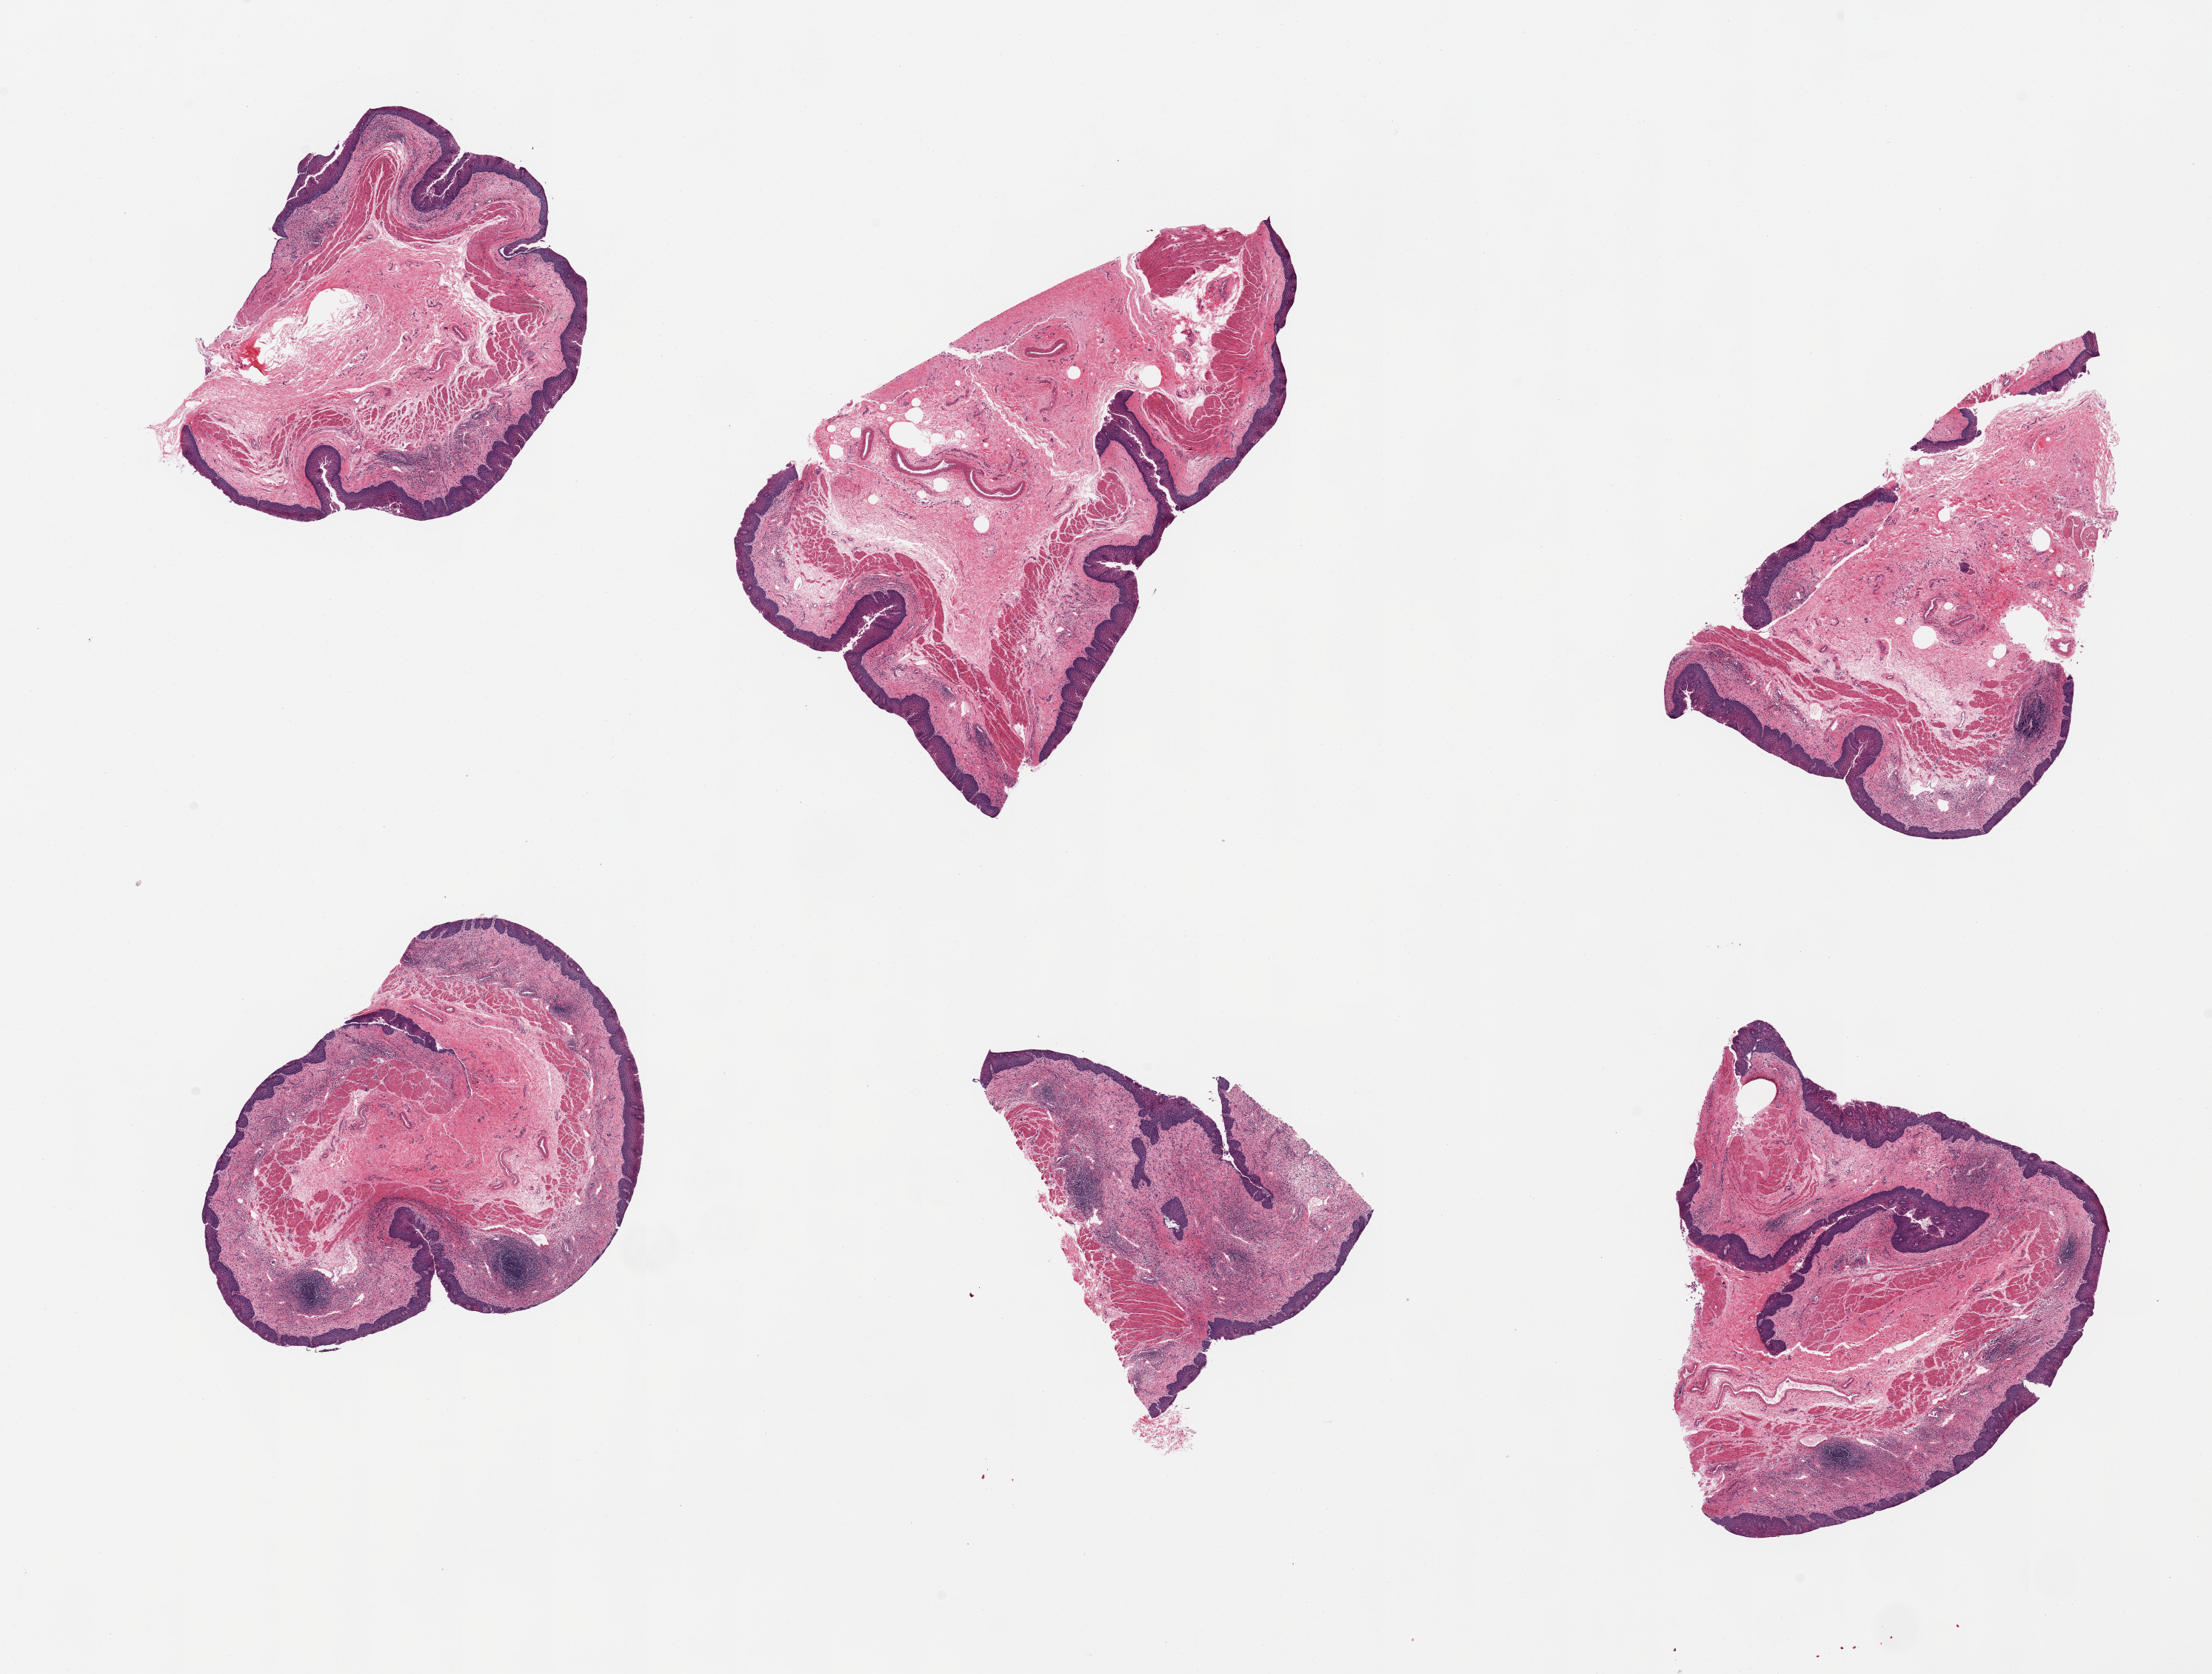
Whole-slide image, H&E stain, brightfield — low-resolution overview of the scanned area, about 23.6 x 17.9 mm (from a 20x scan); PAXgene-fixed paraffin-embedded (PFPE) section; target tissue: esophageal mucous membrane; donor tissue sample. Donor sex: male.
* pathologist's review note for this sample: 6 pieces; chronic inflammation and squamous hyperplasia consistent with reflux